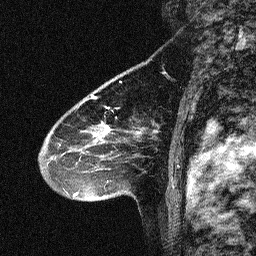
Breast MRI (dynamic contrast-enhanced), one sagittal slice. Slice 43 of 64 in the series (ordered by position). Dynamic contrast-enhanced study with each time point stored as its own series, time point 2 of 3 at this slice position (early post-contrast, ordered by acquisition time). 1.5 T. TE 4.5 ms, TR 11 ms. 2.06 mm slice thickness. 256 × 256 image matrix, field of view 200 × 200 mm. Female patient, age 46 years. From the clinical record (not read from this slice): setting: breast cancer imaged before/during neoadjuvant chemotherapy; receptor status: HER2-positive.
Outlined on this slice (semi-automatic segmentation, software-assisted and operator-edited):
- analysis volume of interest (the breast-tissue region the enhancement analysis was run in; not a lesion): bounding box (x1, y1, x2, y2) in pixels: (42, 80, 150, 180)
- tumour enhancement mask (voxels above the 90 % enhancement threshold inside the analysis volume of interest): (80, 126, 142, 163)